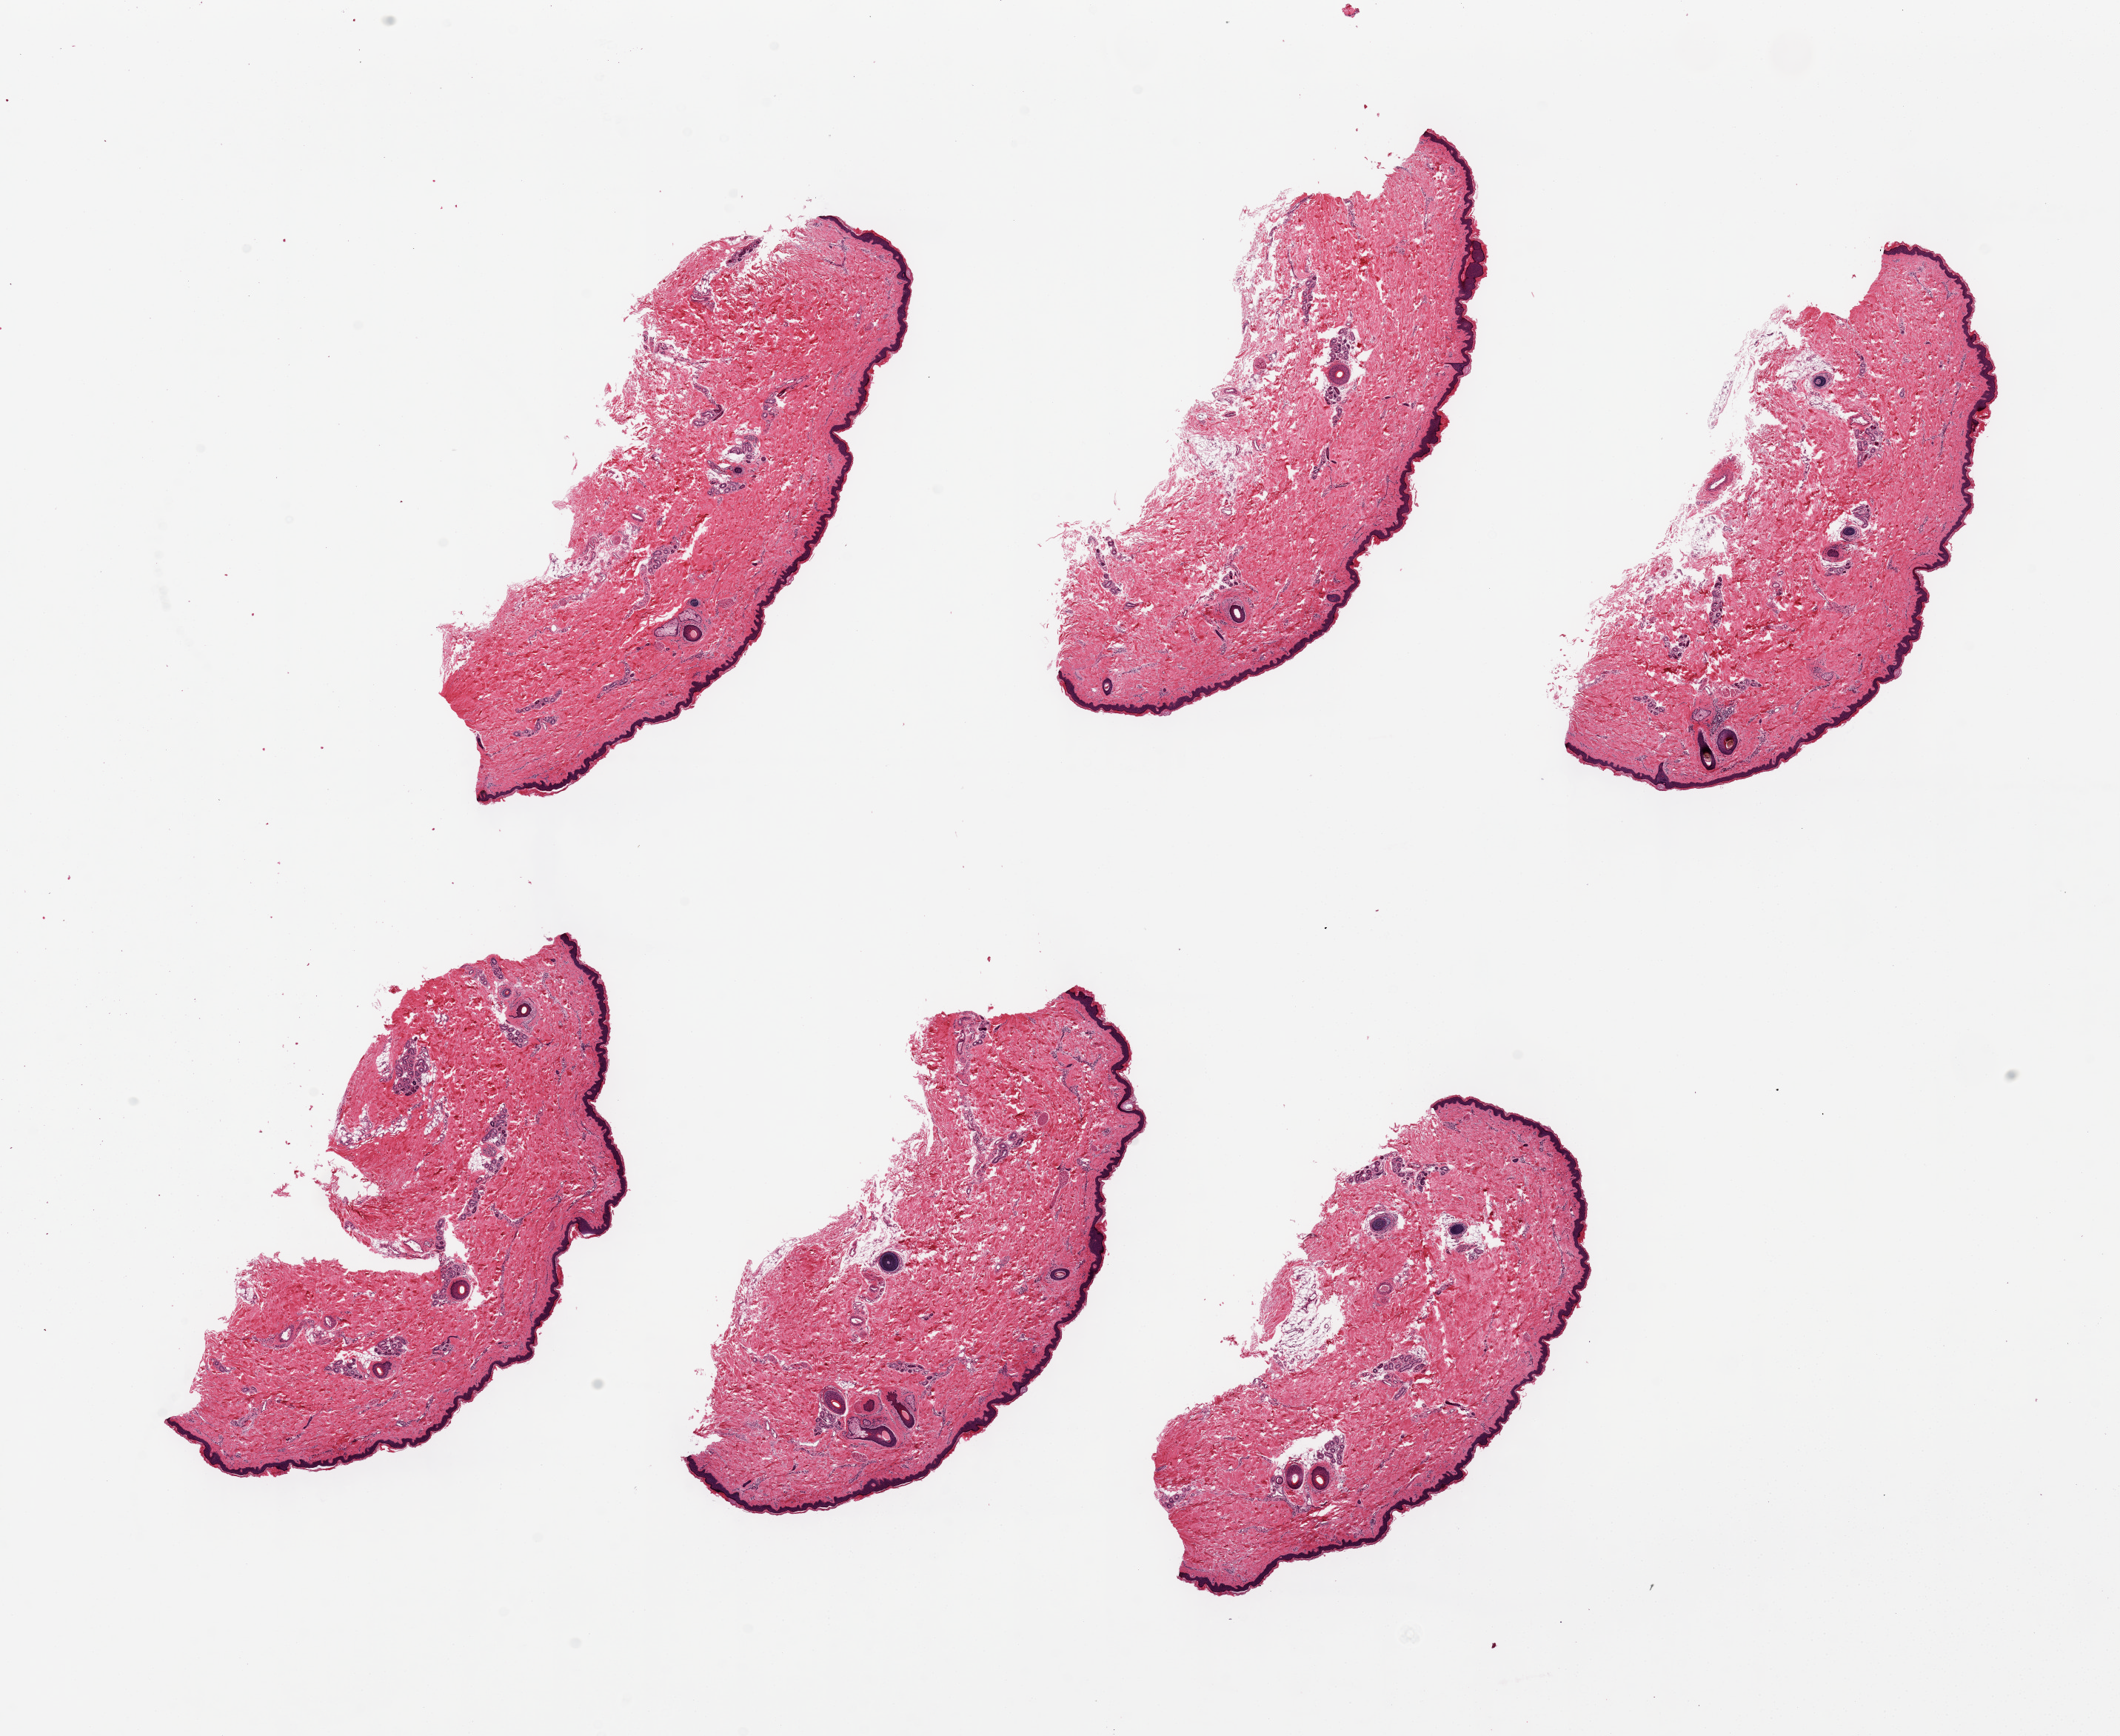
Haematoxylin and eosin whole-slide image, a low-resolution overview of the entire scanned area, about 22.6 x 18.5 mm, PAXgene-fixed, paraffin-embedded tissue, section of skin of lower leg (target tissue), tissue donor sample. Donor: male.
Reviewer comment on this tissue sample: 6 pieces up to 7x3 mm.